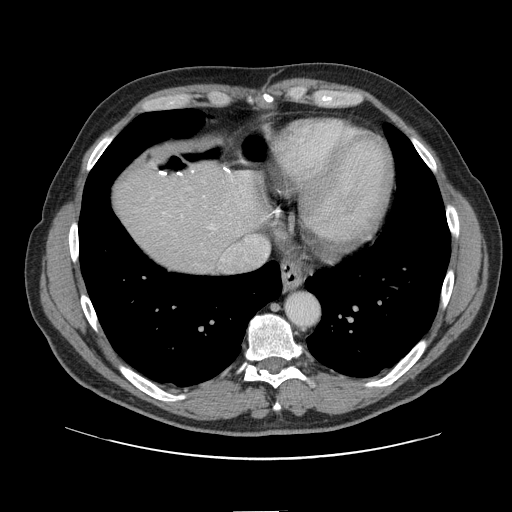
Contrast-enhanced abdominal CT, one axial slice; slice 133 of 161 in the series (ordered by position); 120 kVp; intravenous contrast given; soft-tissue window (W 400 / L 40 HU); 512 × 512 image matrix, field of view 412 × 412 mm. Male patient, age 66 years. From the clinical record (not read from this slice): diagnosis: colorectal cancer liver metastases, imaged before liver resection; multiple liver metastases: no.
Outlined on this slice (manually delineated by an expert):
- hepatic veins: box from (x=182, y=197) to (x=236, y=262) px
- liver: (x=115, y=165)–(x=263, y=273)
- planned liver remnant (the part of the liver to remain after resection): (x=115, y=165)–(x=262, y=272)